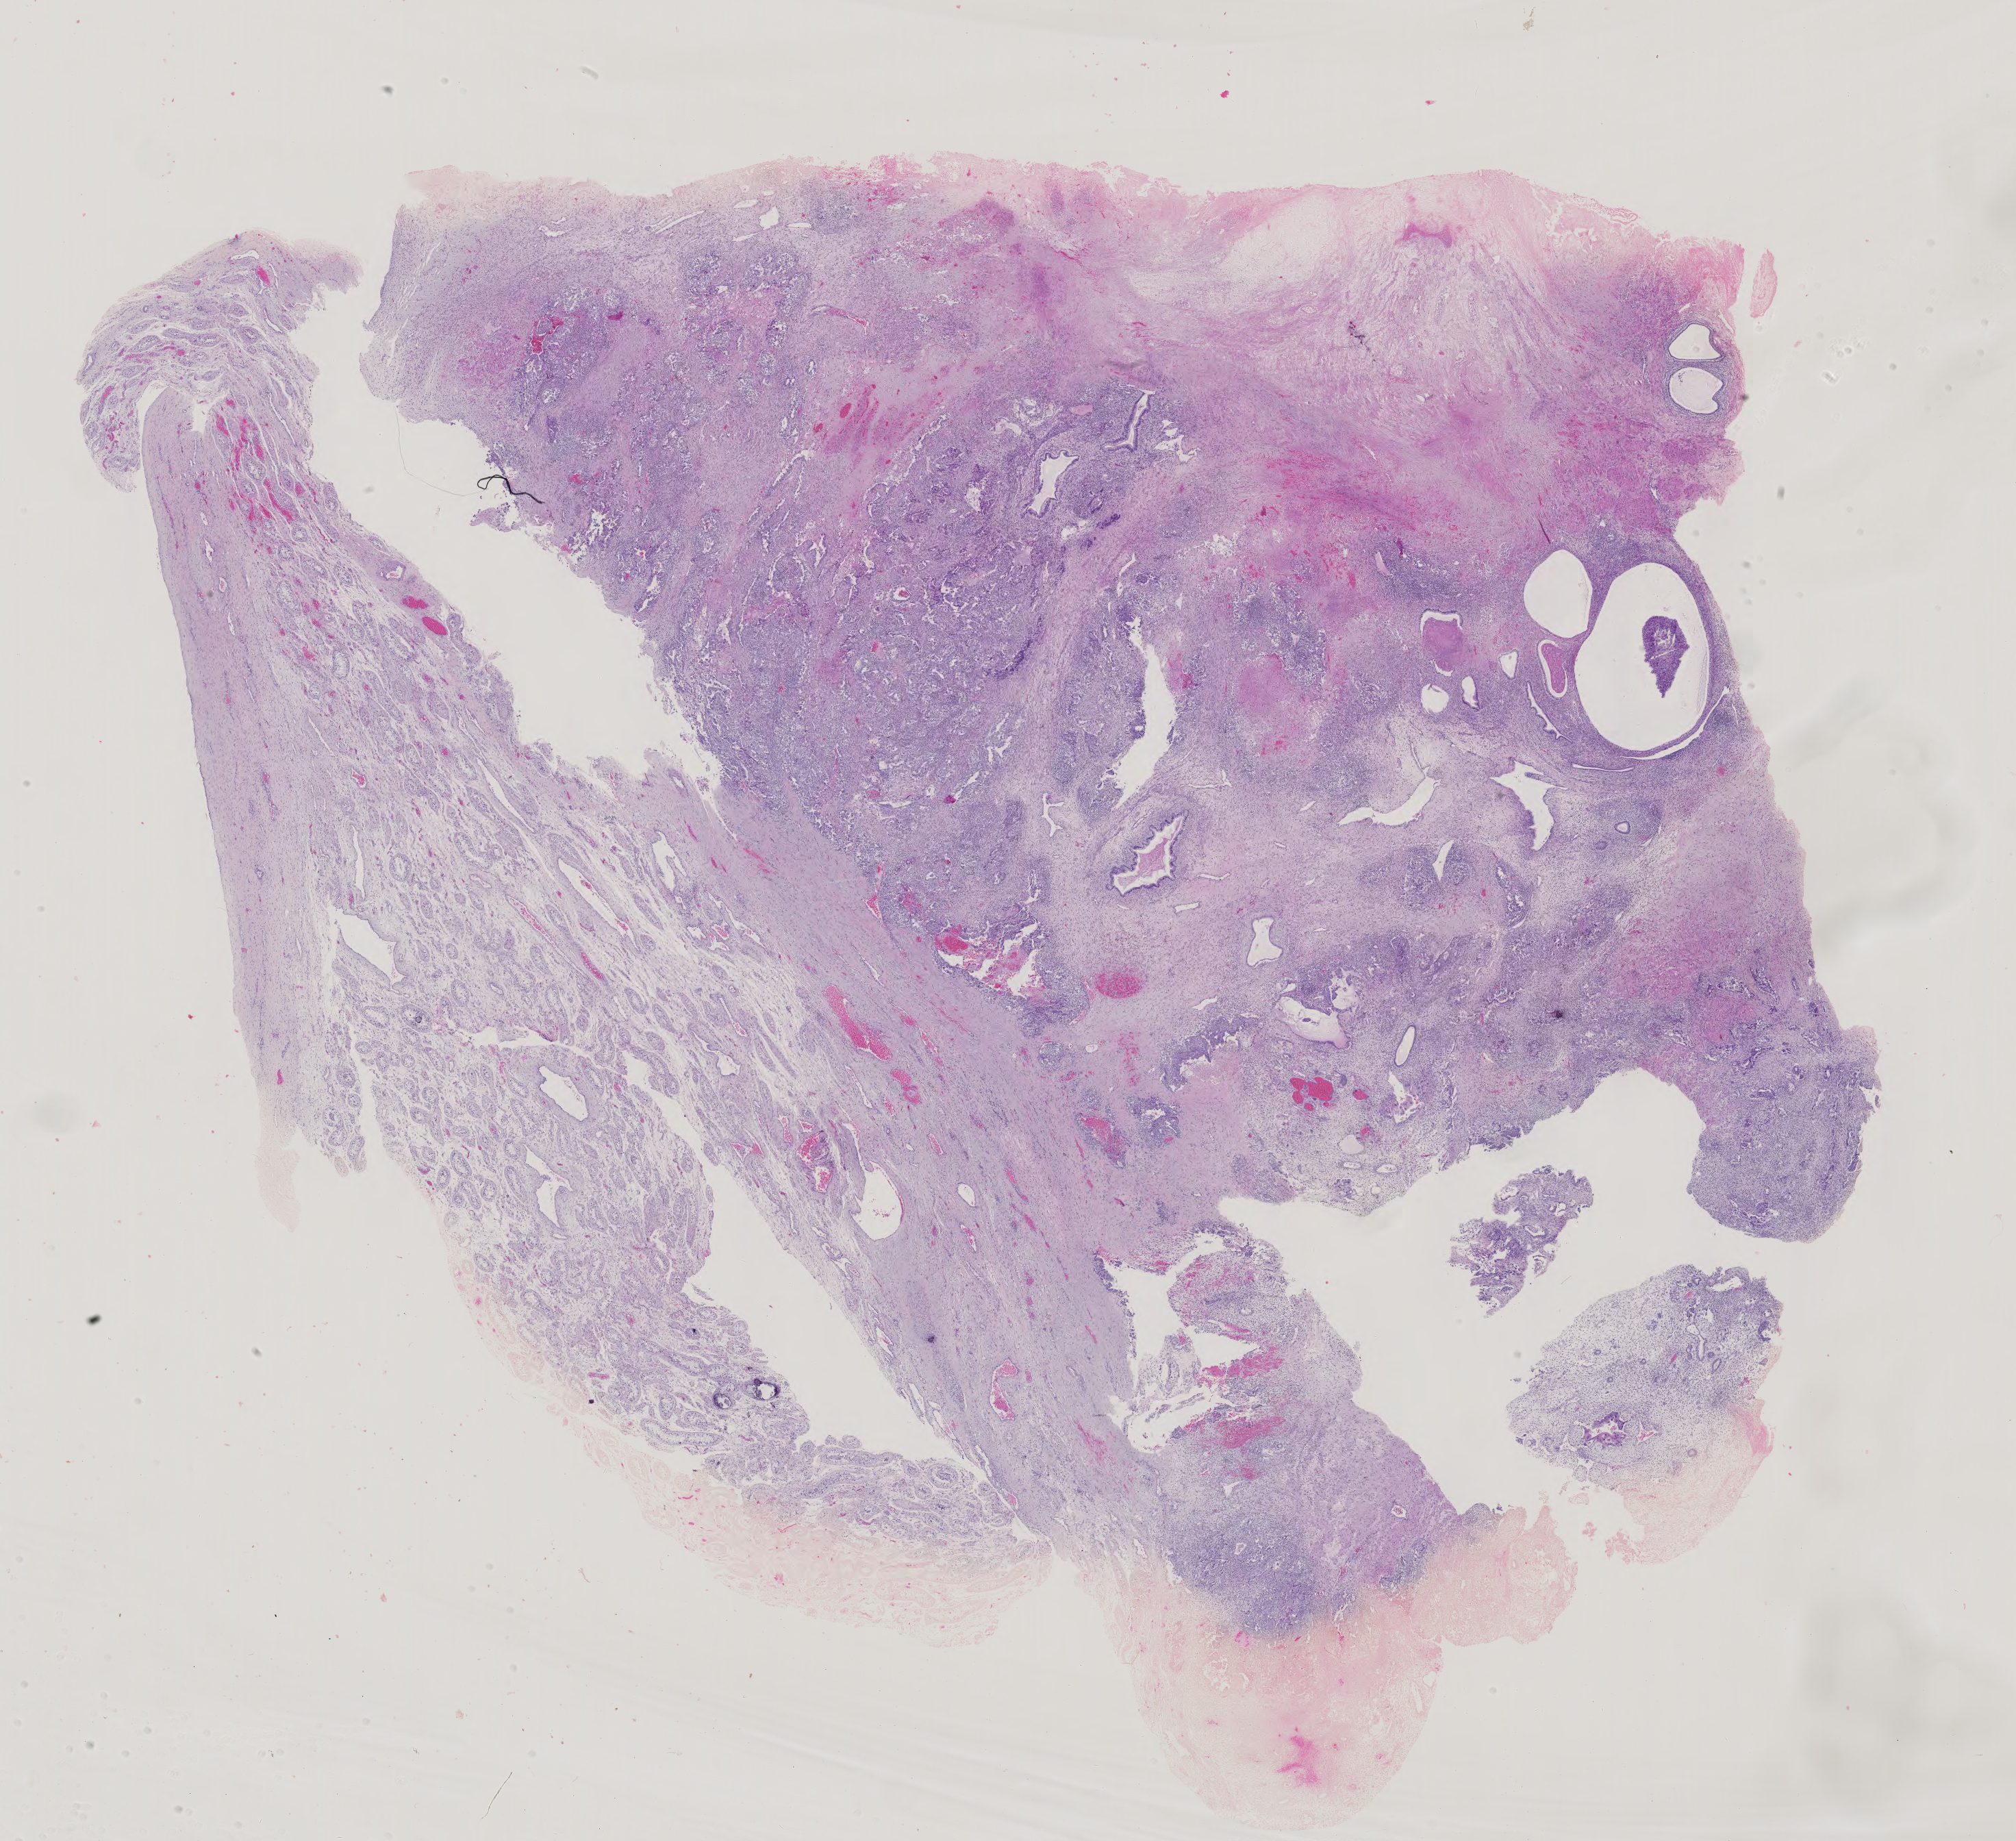
Digitized H&E-stained tissue section (whole slide) — low-resolution overview of the scanned area, about 21.5 x 19.6 mm, formalin-fixed paraffin-embedded (FFPE) diagnostic section, sample: primary tumour, testis. Patient: male, age at initial diagnosis 22 years.
* AJCC pathologic stage: I
* pathologic diagnosis: Embryonal carcinoma, NOS
* laterality: left